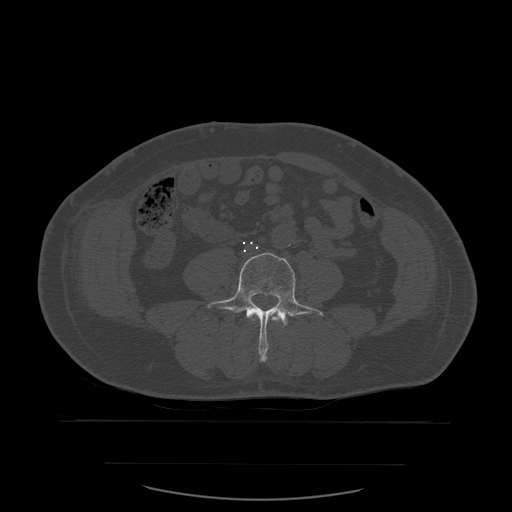
CT including the spine, one axial slice. Slice 168 of 590 in the series (ordered by position). Bone window (W 1800 / L 400 HU). 1.25 mm slice thickness. 512 × 512 image matrix. Patient age 71 years. From the clinical record (not read from this slice): primary cancer: lung.
Annotated regions visible in this slice (semi-automatically segmented with operator editing):
- L3 vertebra: bounding box (x1, y1, x2, y2) in pixels: (249, 312, 285, 325)
- L4 vertebra: (208, 253, 324, 362)